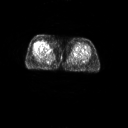
FDG PET of an extremity soft-tissue mass (from a PET/CT study), one axial slice. Position 12 of 267 along the scan axis. 3.27 mm slice thickness. 128 × 128 image matrix. Patient: female, 56 years. From the clinical record (not read from this slice): histological type: malignant solitary fibrous tumor; grade: intermediate; site of the primary tumour: right thigh.
Structures marked on this image (expert contour drawn on MRI and transferred to this co-registered scan by the dataset authors):
- gross tumour volume including surrounding oedema: bounding box <42,41,51,48> (left, top, right, bottom; pixels)